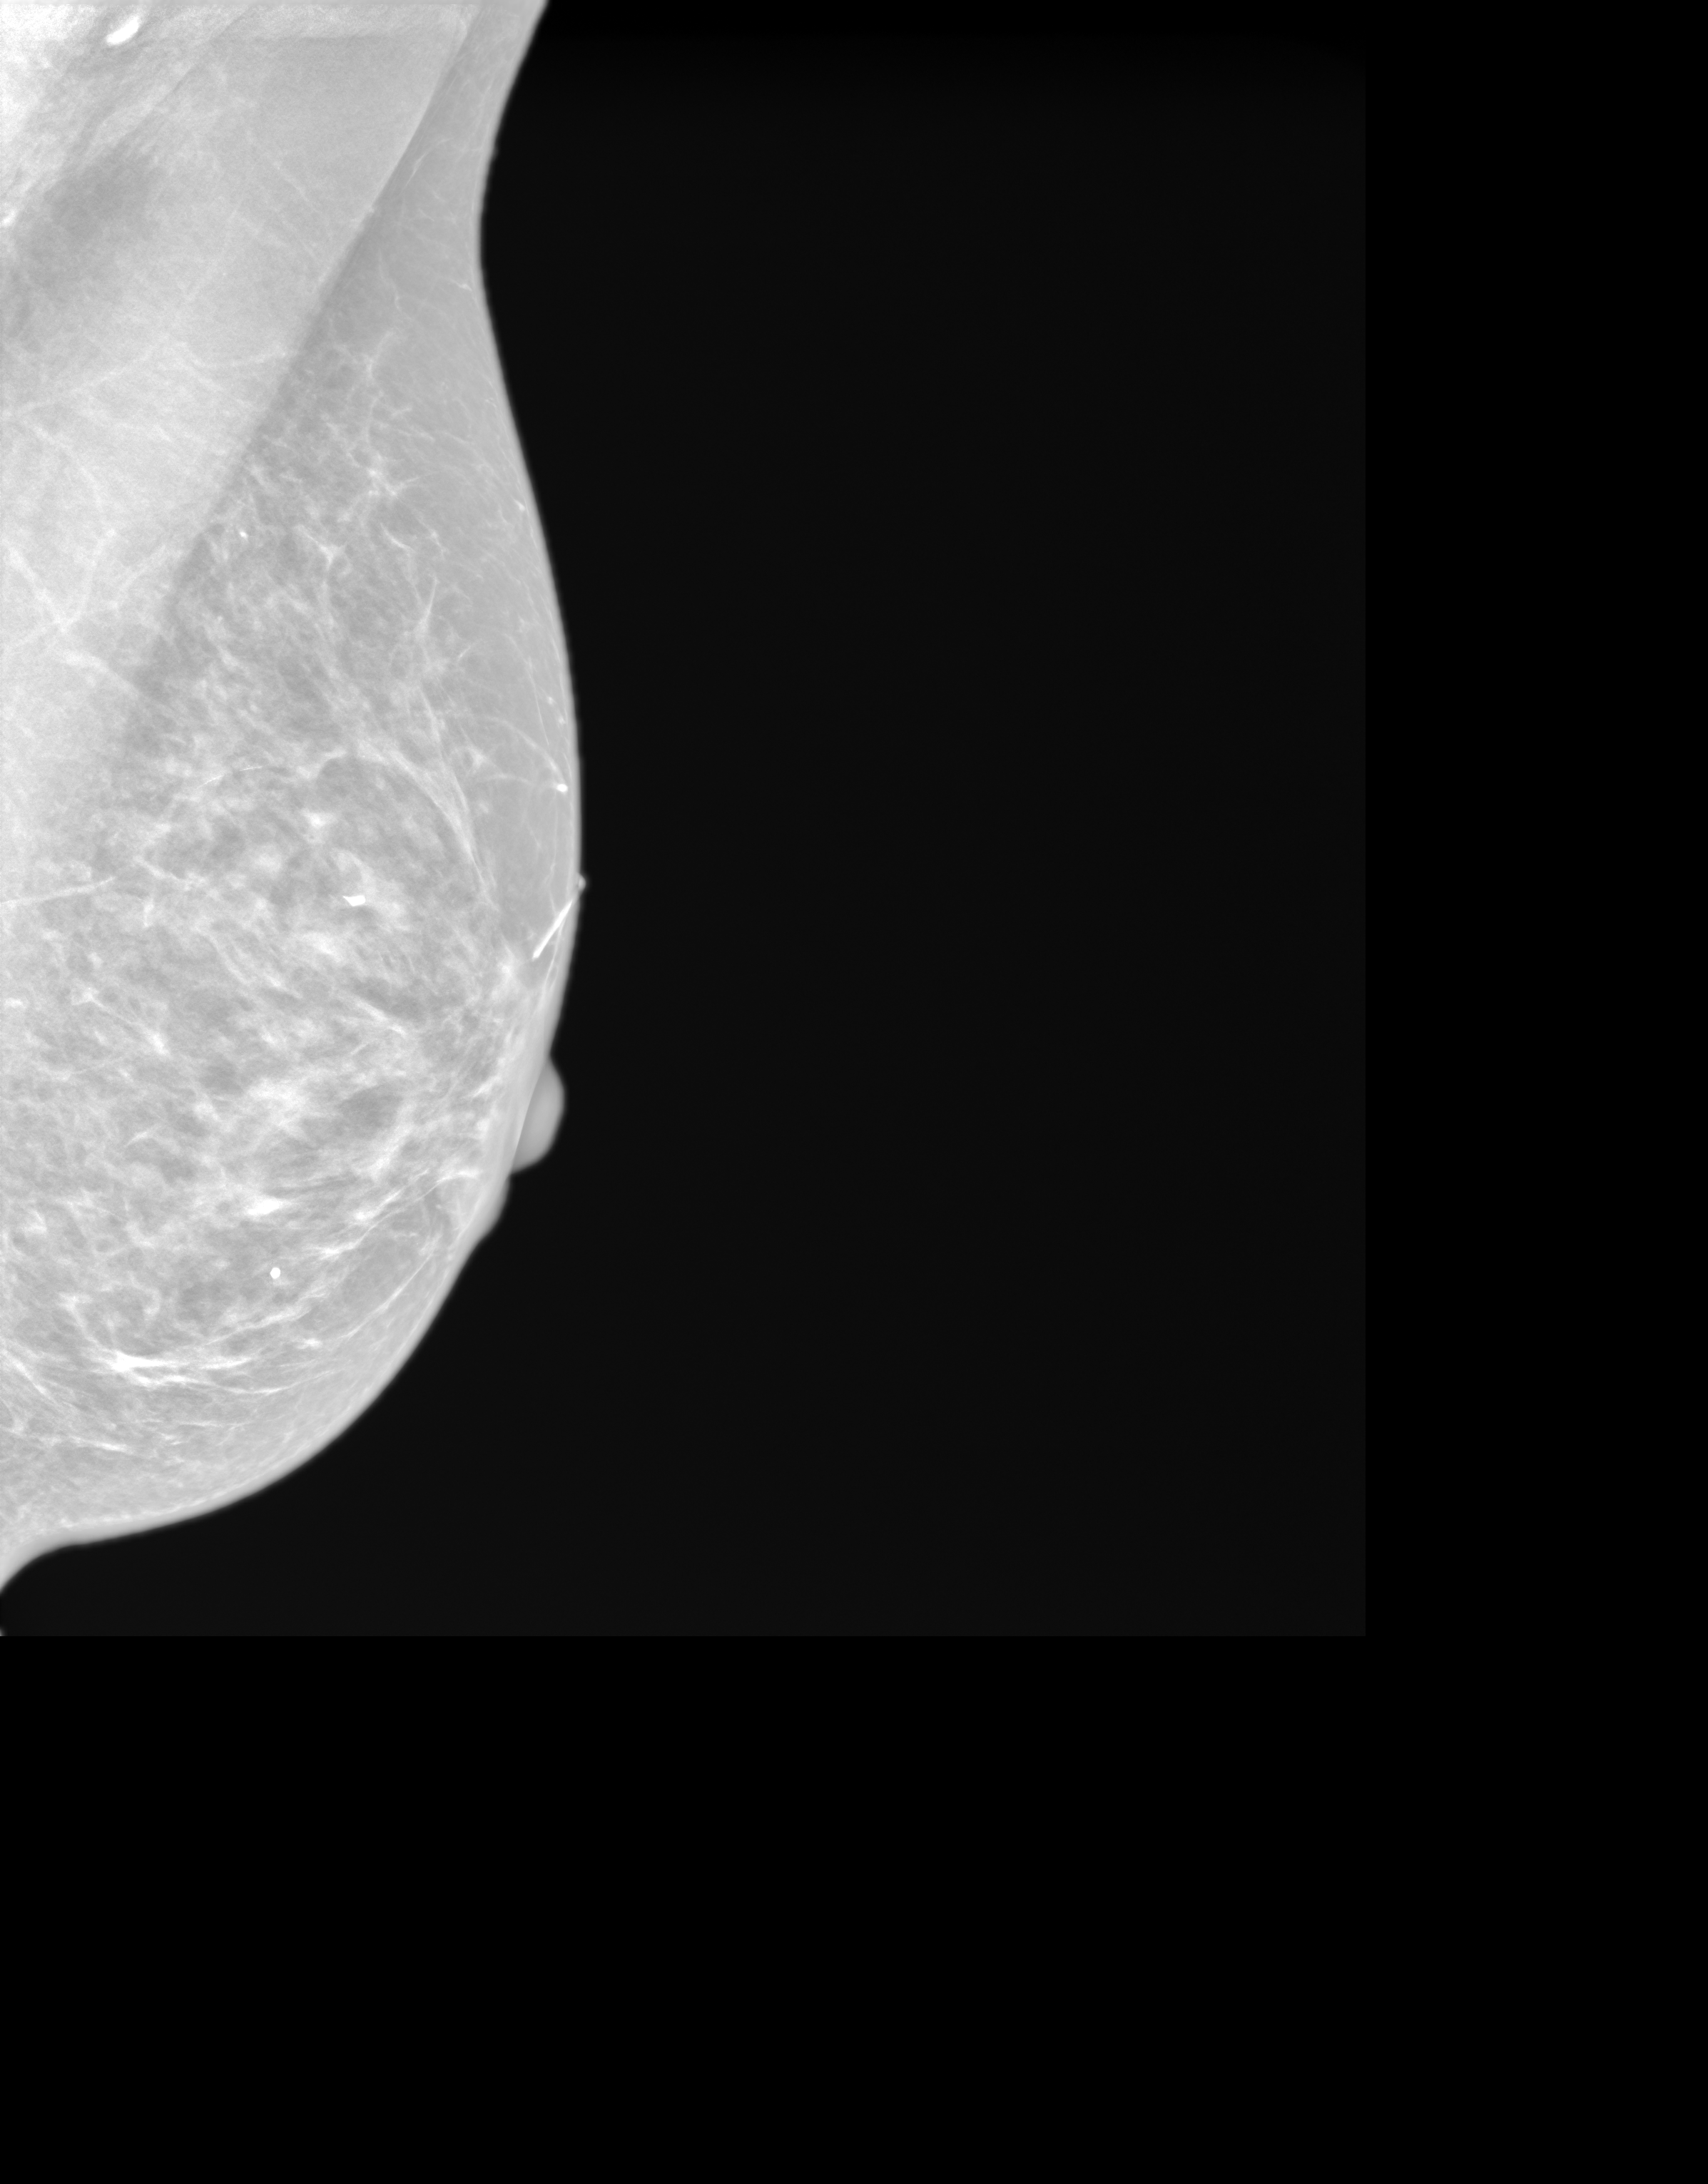
Annual screening mammography examination. Female patient, age 70 years.
Image type: synthesized 2-D view from tomosynthesis. Breast: left. Projection: MLO view.